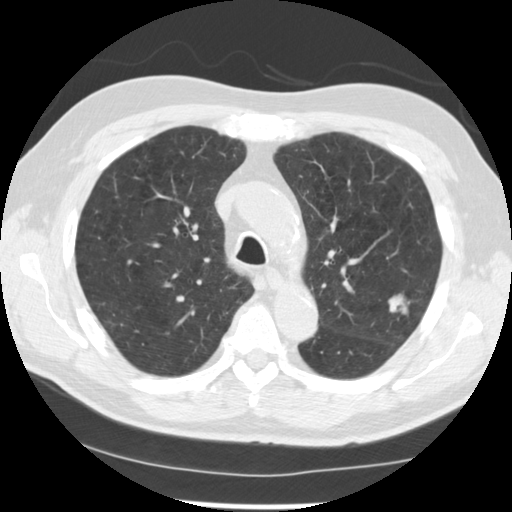
Low-dose screening chest CT, one axial slice. Slice 175 of 249 in the series (ordered by position). 120 kVp. Lung window (W 1500 / L -600 HU). 2.5 mm slice thickness. 512 × 512 image matrix, field of view 341 × 341 mm.
Outlined on this slice (outlined manually by an expert reader):
- lesion 1 (tumor, upper lobe of left lung): bounding box [x1, y1, x2, y2] px = [389, 295, 408, 313]